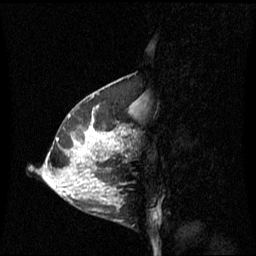
Breast MRI (dynamic contrast-enhanced), one sagittal slice. Slice 23 of 60 in the series (ordered by position). Dynamic contrast-enhanced series, image 2 of 3 at this slice position (ordered by acquisition). 1.5 T. TE 4.2 ms, TR 8.4 ms. 2.1 mm slice thickness. 256 × 256 image matrix, field of view 240 × 240 mm. Female patient, age 42 years. From the clinical record (not read from this slice): setting: breast cancer imaged before/during neoadjuvant chemotherapy; receptor status: HR-positive, HER2-negative.
Outlined on this slice (semi-automatically segmented with operator editing):
- analysis volume of interest (the breast-tissue region the enhancement analysis was run in; not a lesion): box from (x=68, y=100) to (x=137, y=201) px
- tumour enhancement mask (voxels above the 70 % enhancement threshold inside the analysis volume of interest): (x=92, y=118)–(x=125, y=135)